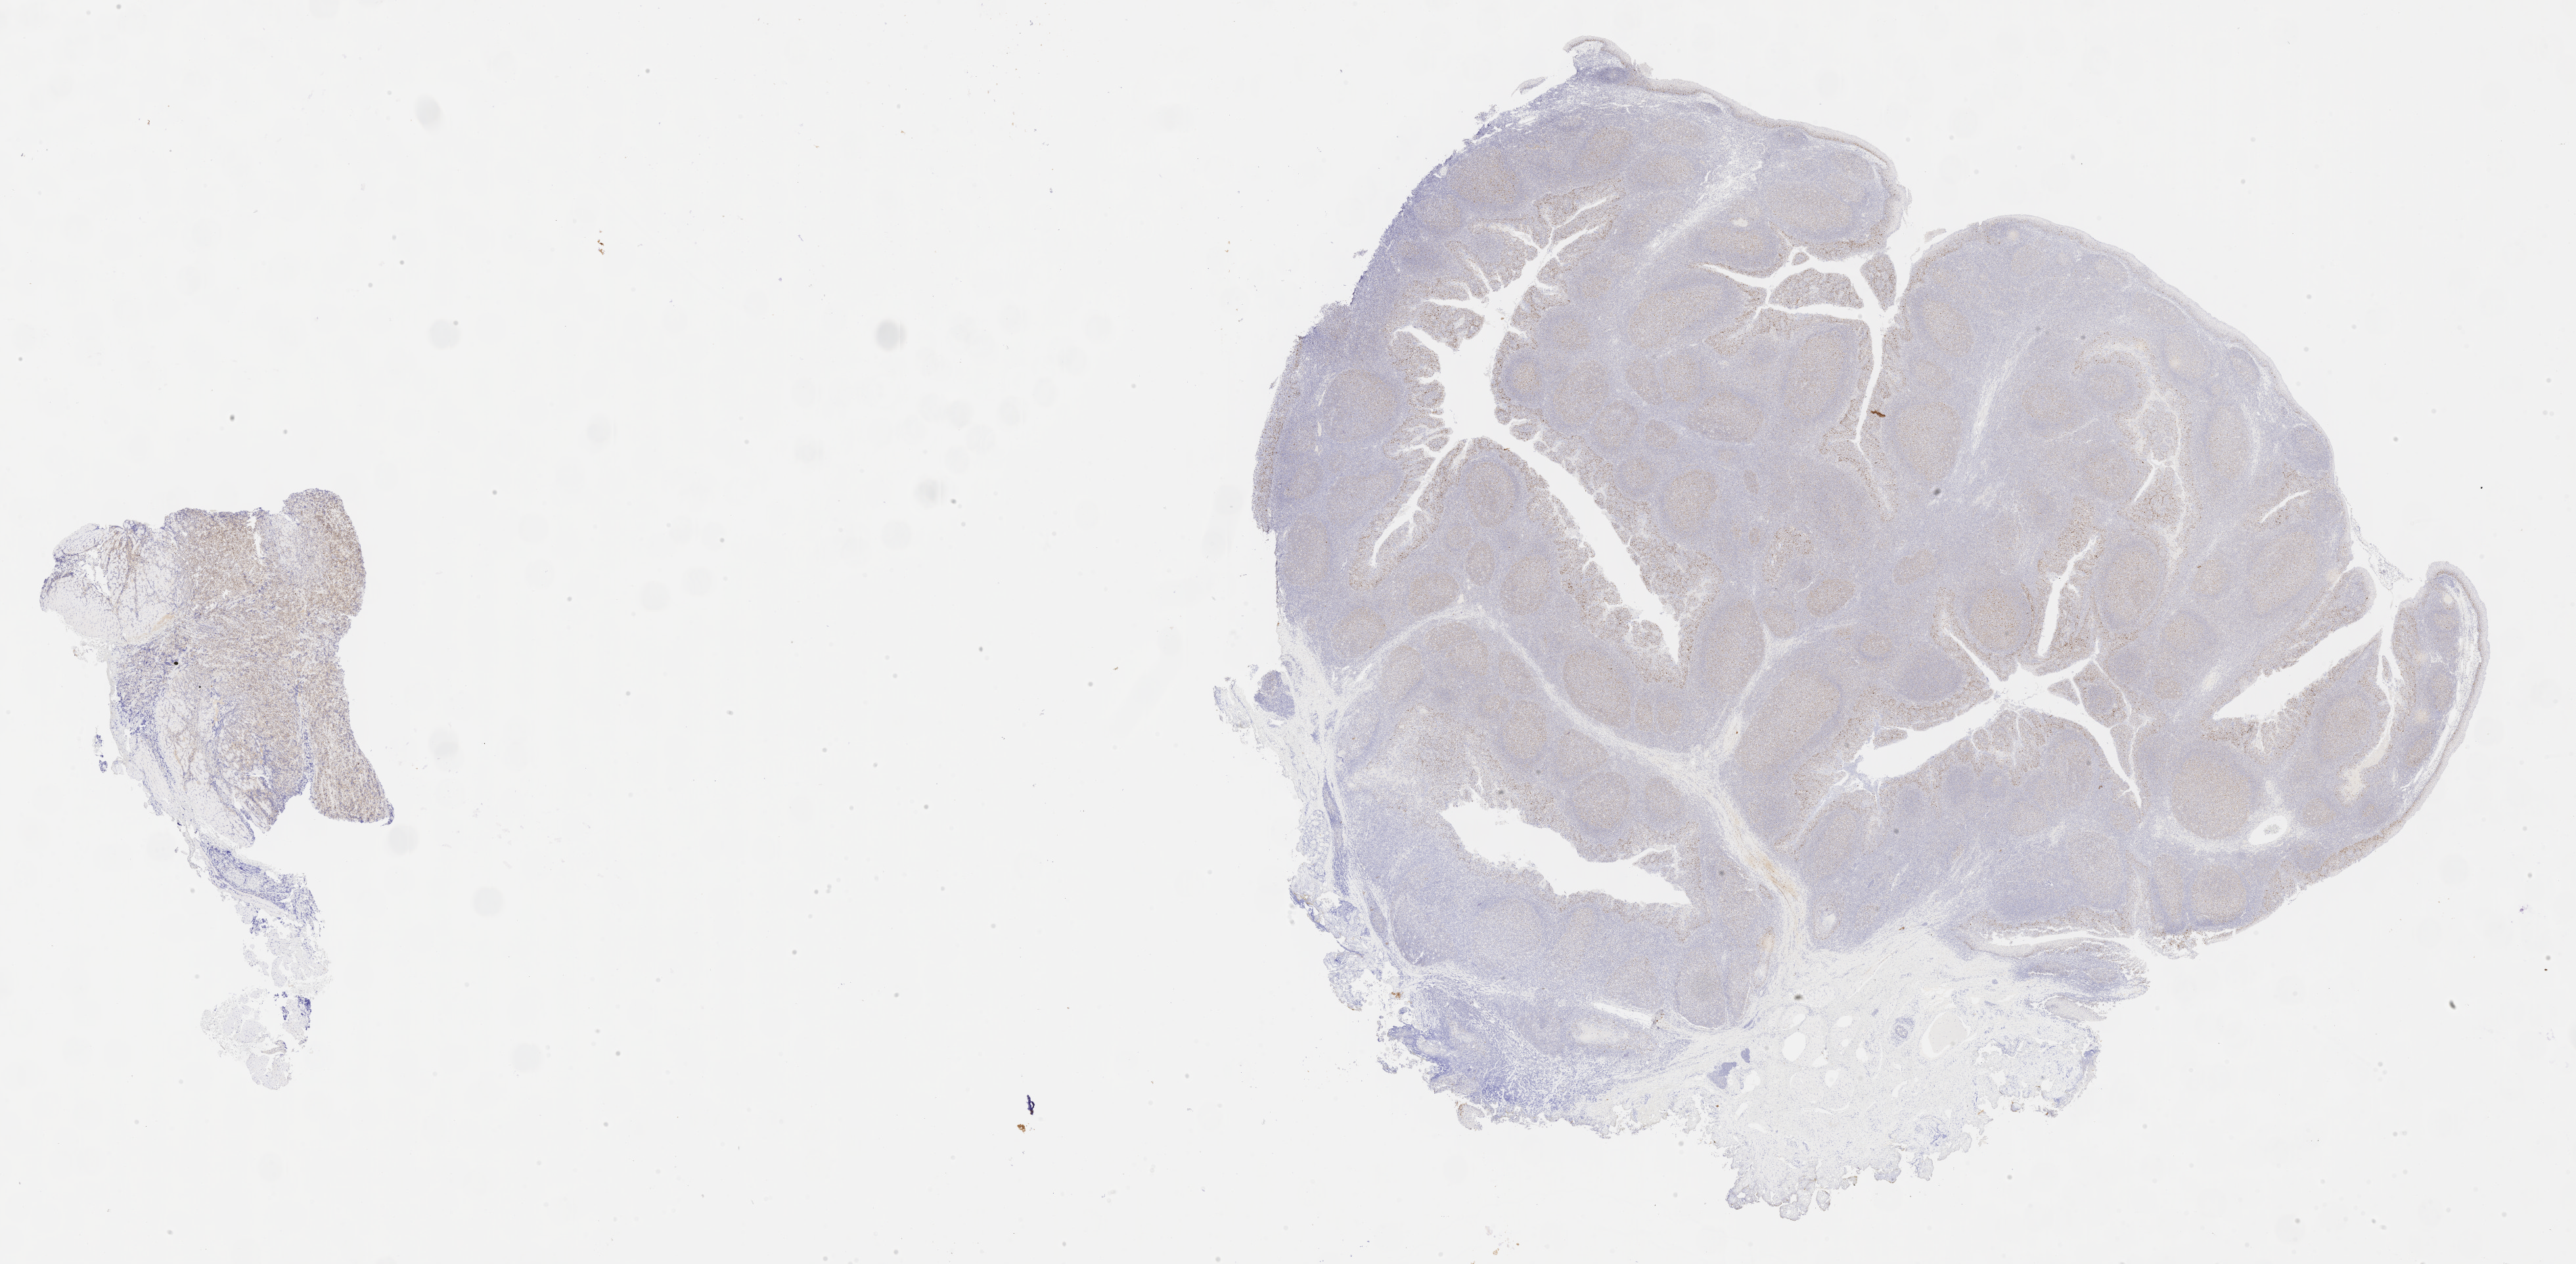
Immunohistochemistry (IHC) whole-slide image stained for p53 — a low-resolution overview of the entire scanned area, about 31.7 x 15.6 mm, tumor tissue, site: kidney. Patient male; aged 12.
Histologic diagnosis: Diffuse large B-cell lymphoma, NOS.